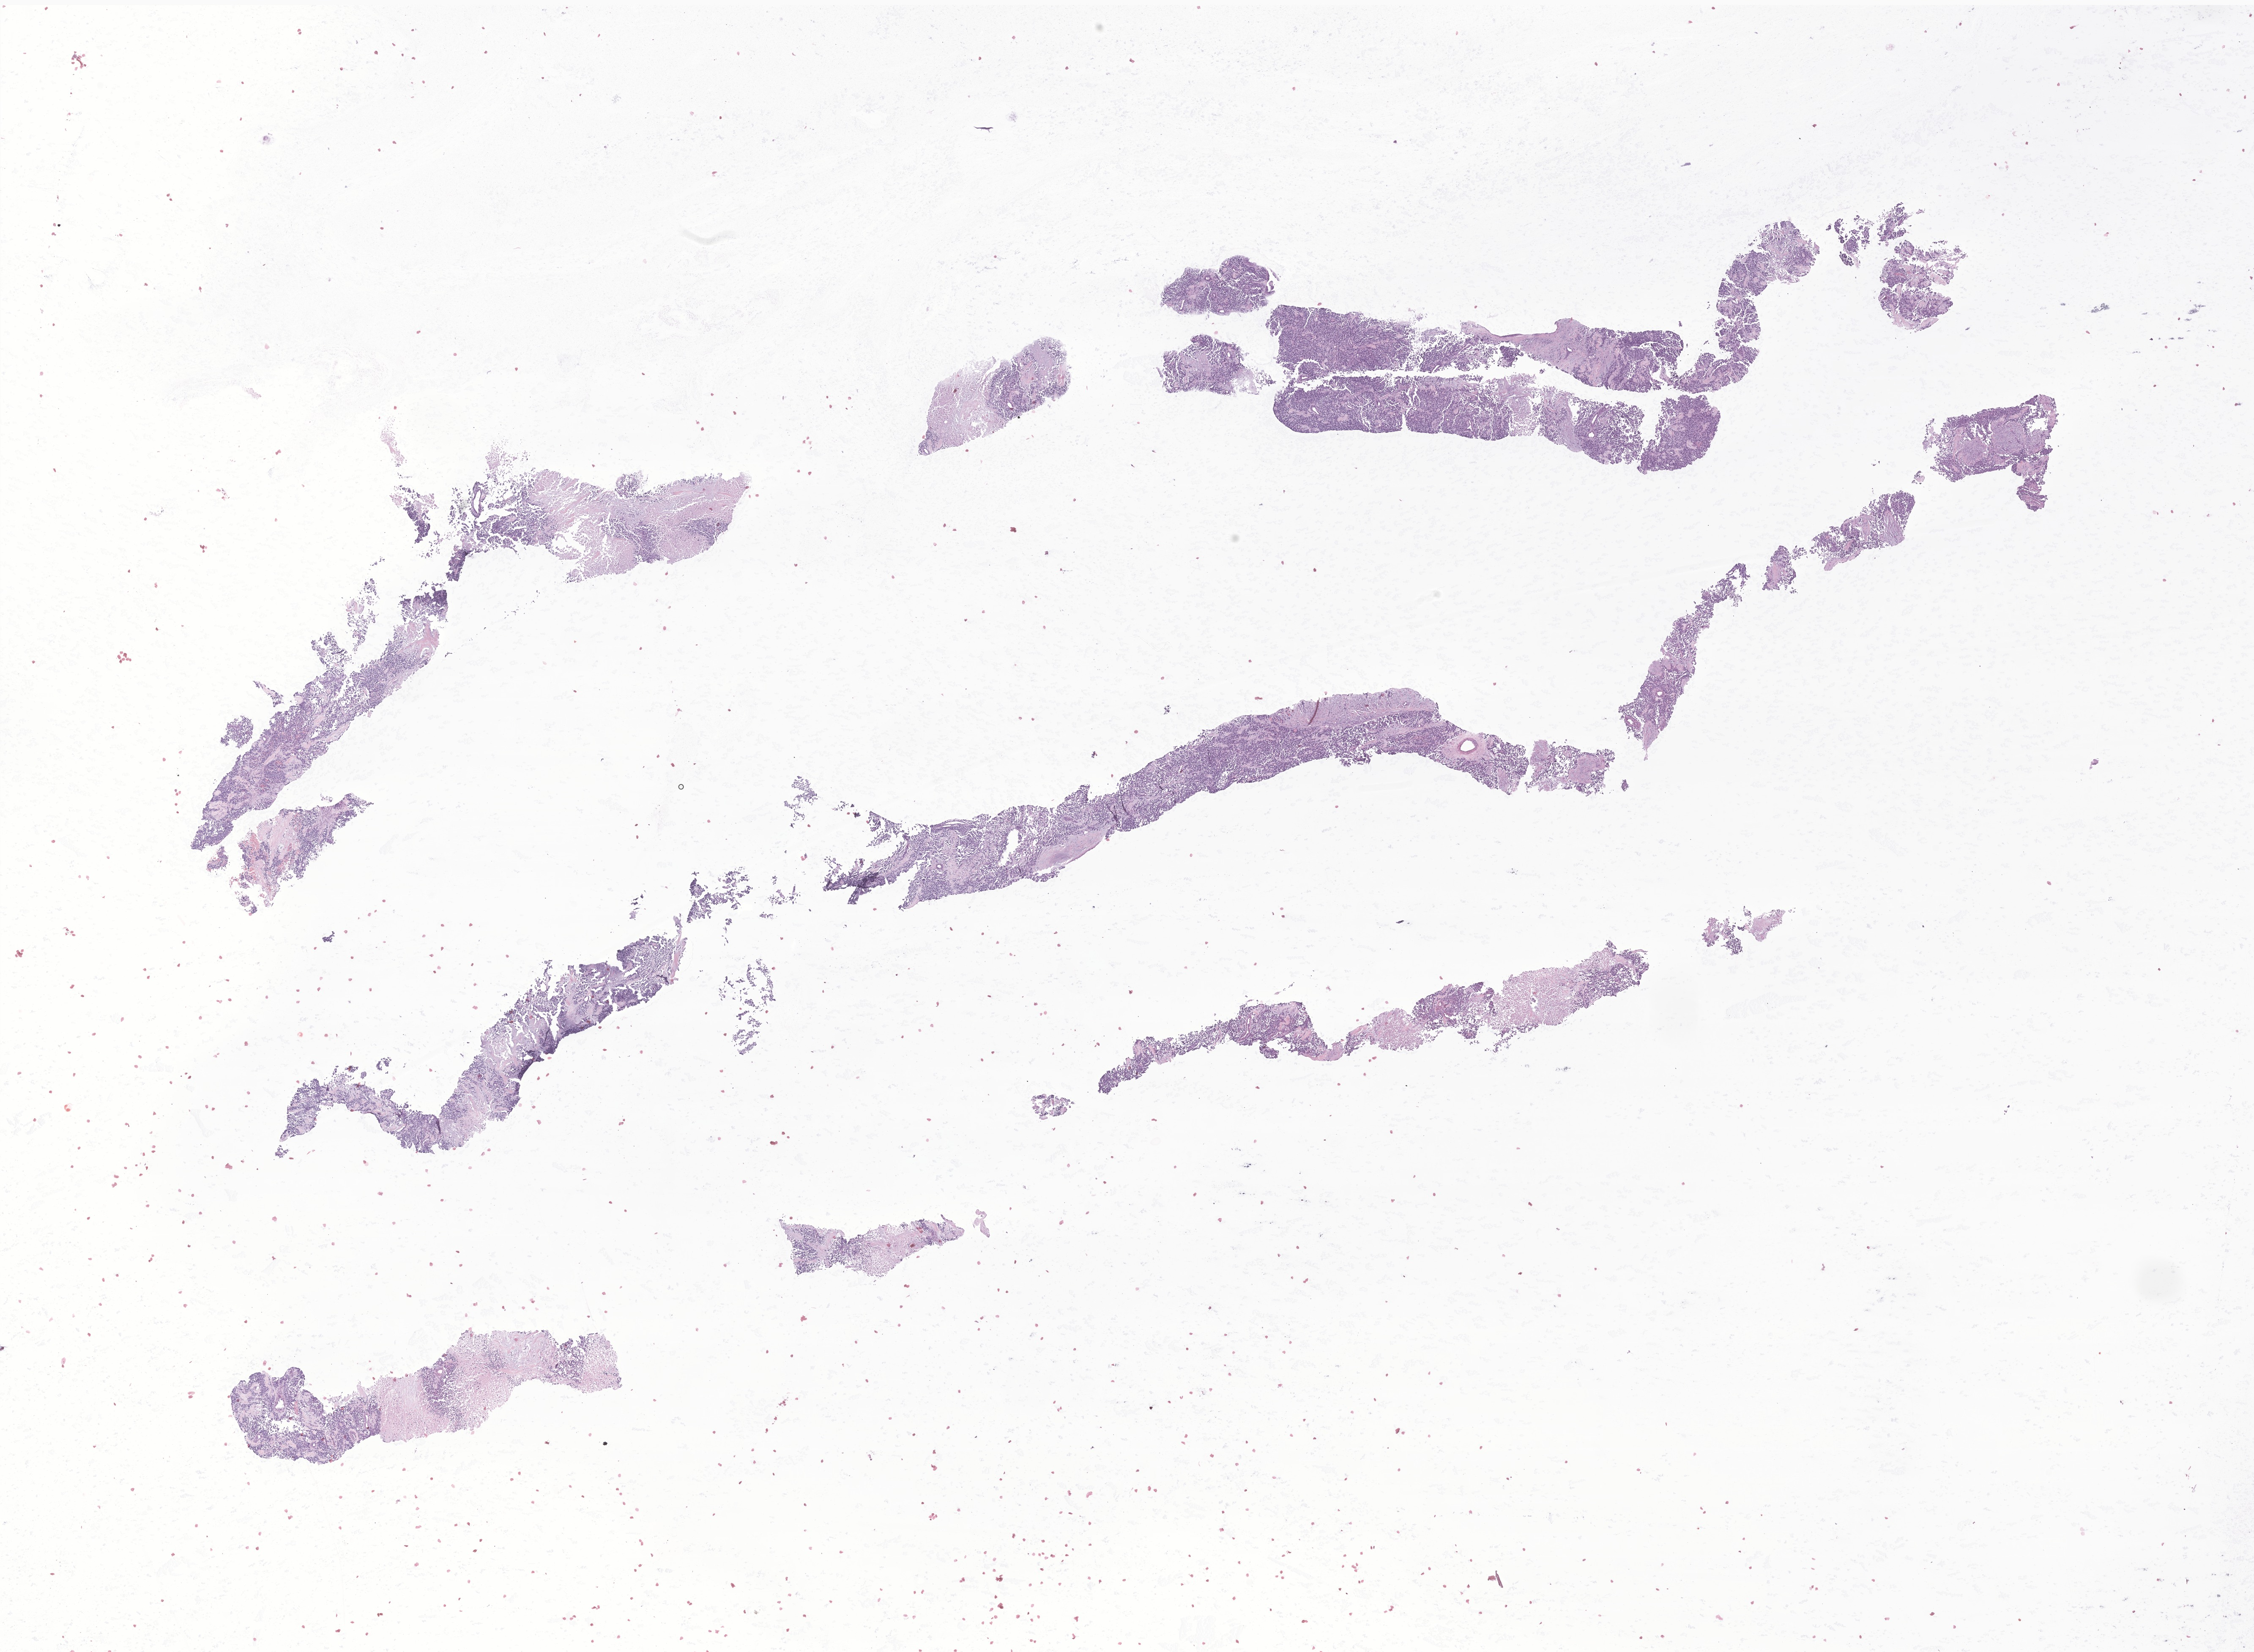
Digitized haematoxylin and eosin-stained section of tumor tissue from the soft tissue of trunk — a low-resolution overview of the entire scanned area, about 22.5 x 16.5 mm, formalin-fixed, paraffin-embedded (FFPE) tissue. Female patient, age 146 months (12 years 2 months).
• recorded diagnosis: Alveolar rhabdomyosarcoma